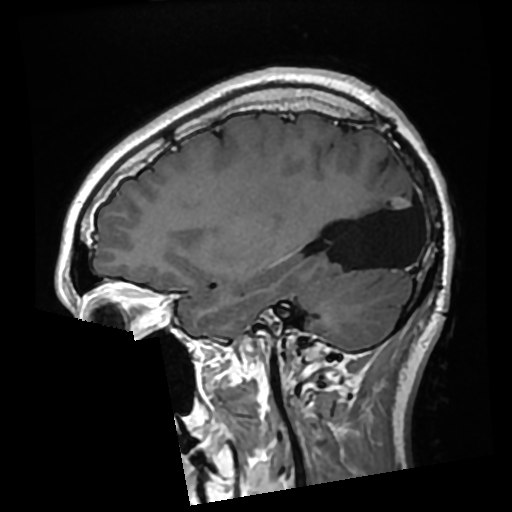
Brain MRI from a brain-tumour surgery series, one sagittal slice; slice 97 of 276 in the series (ordered by position); T1-weighted post-contrast; 0.7 mm slice thickness; 512 × 512 image matrix, field of view 250 × 250 mm. From the clinical record (not read from this slice): histopathology: Glioma with ependymal features; WHO grade: 2.
Structures marked on this image (outlined manually by an expert reader):
- previous resection cavity: bounding box (x1, y1, x2, y2) in pixels: (325, 182, 417, 270)
- tumour: (392, 197, 410, 209)